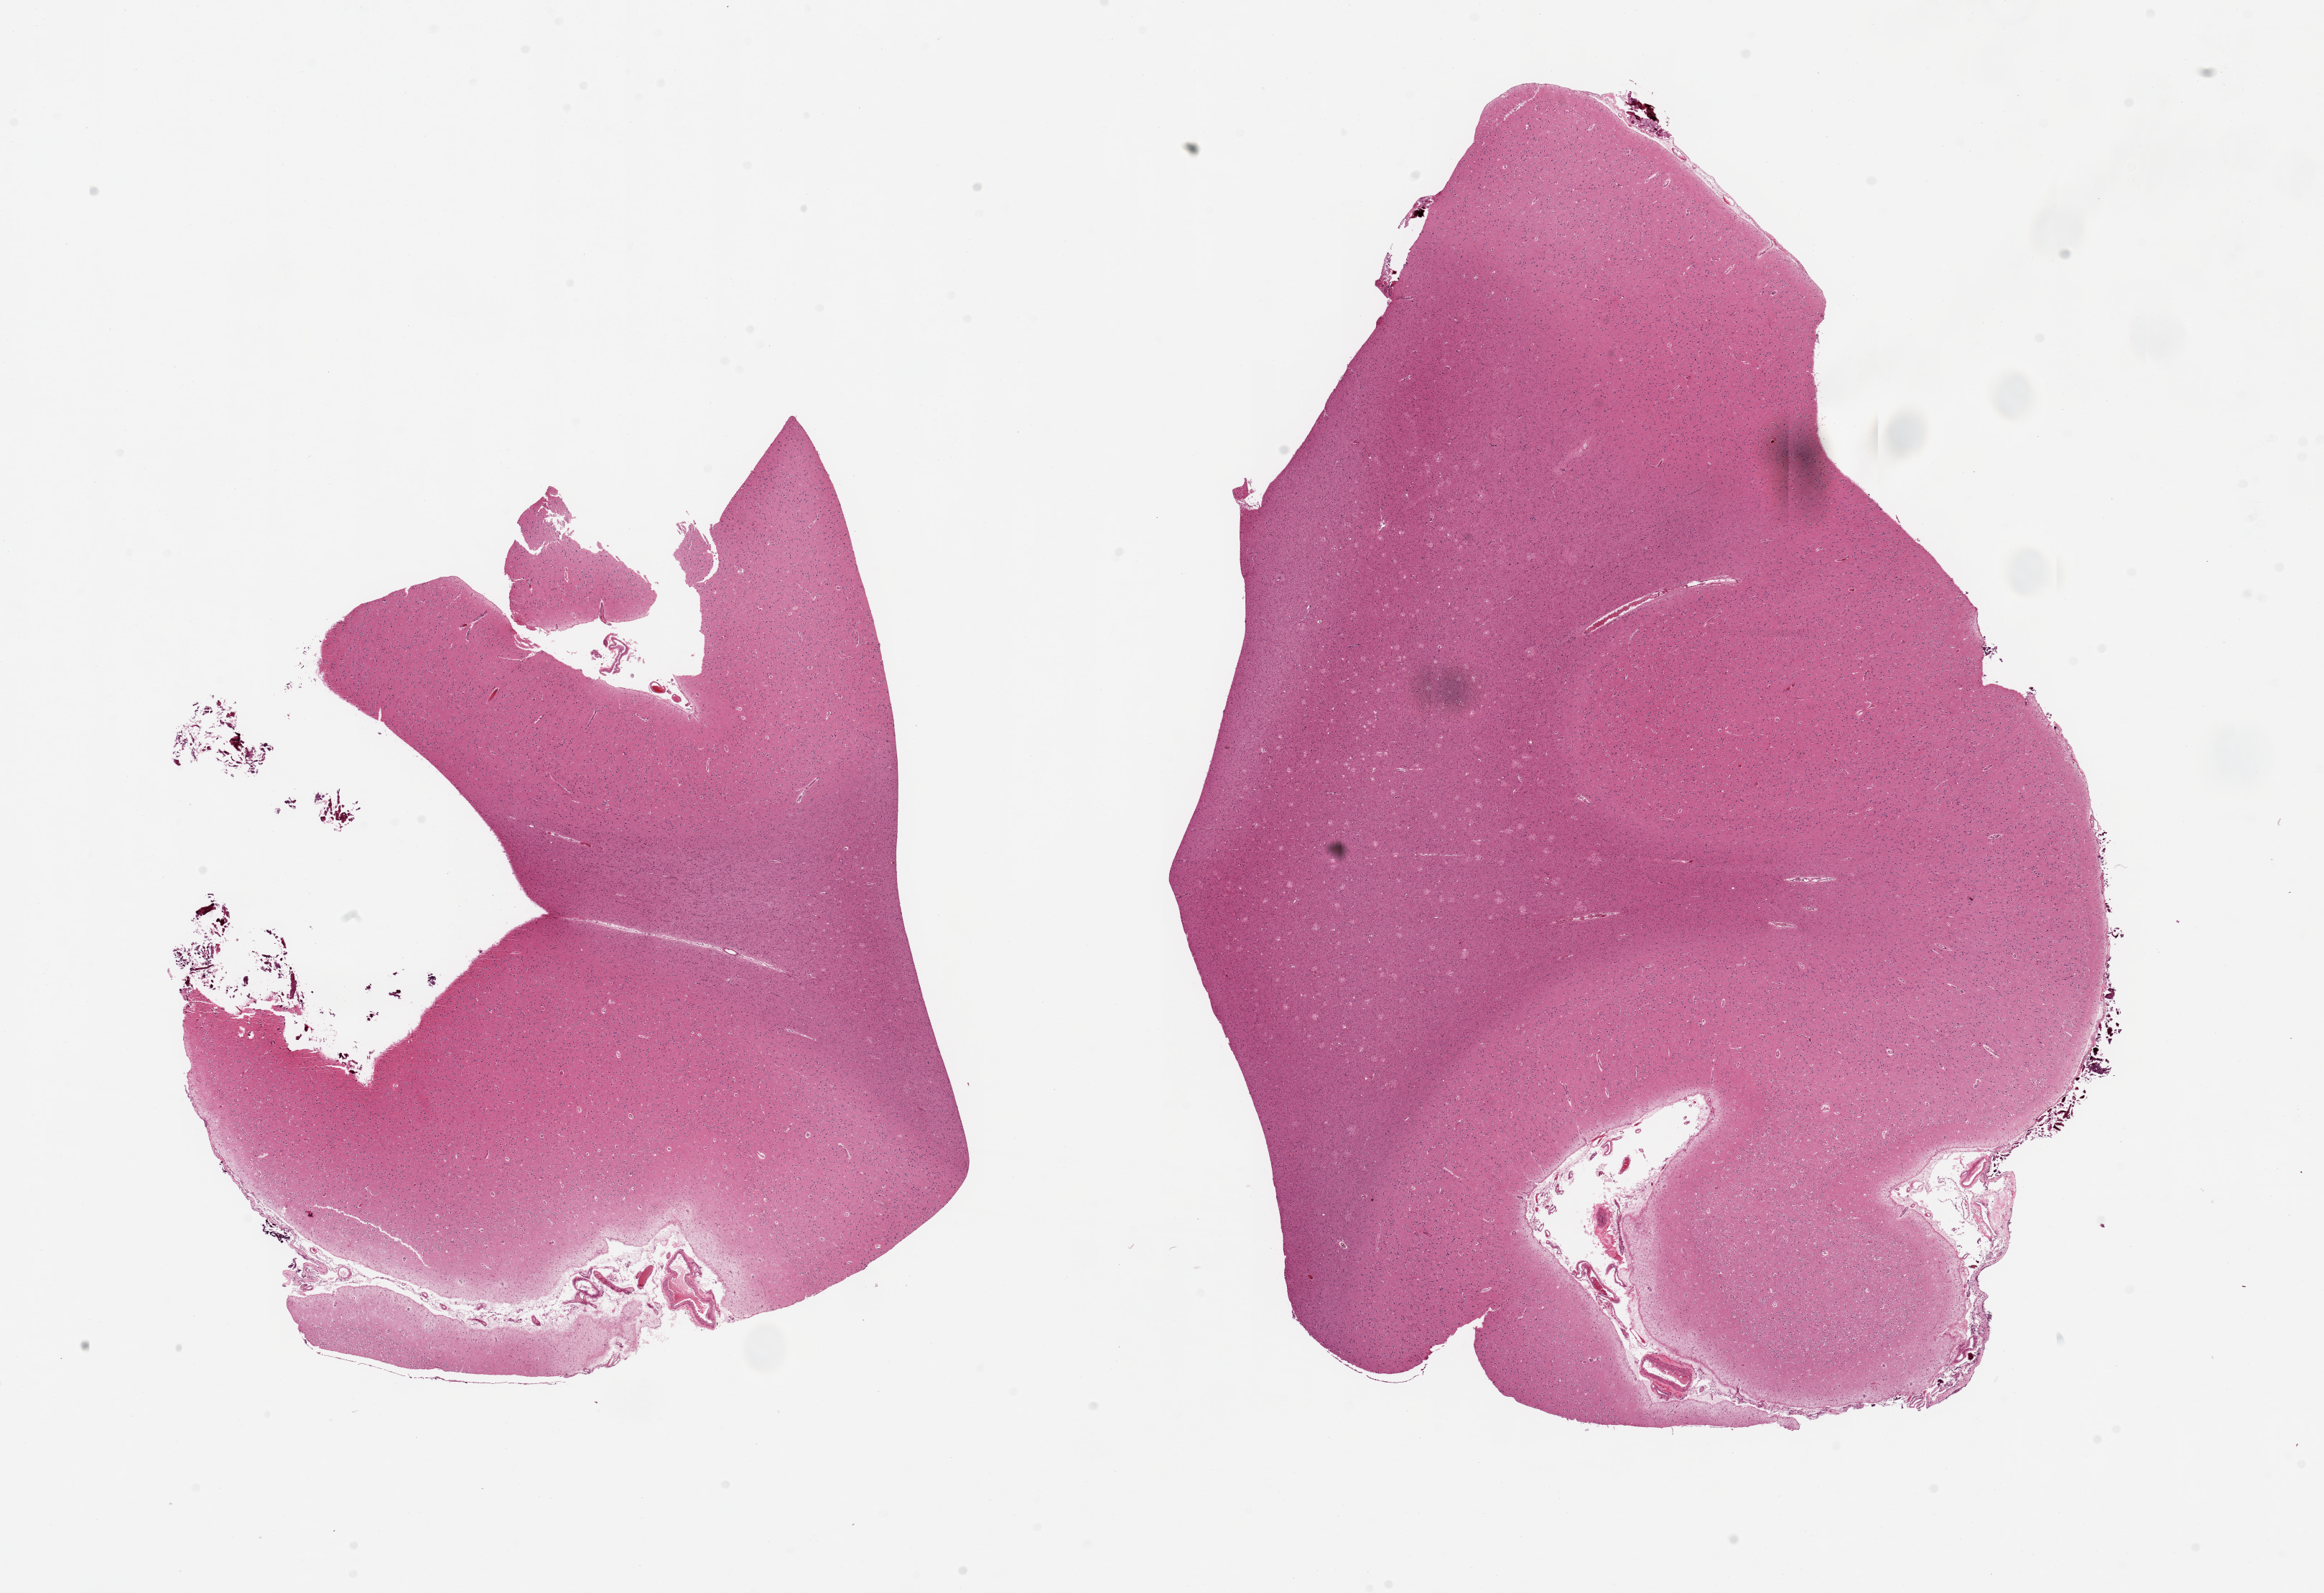
H&E whole-slide image, low-resolution overview of the scanned area, about 25.6 x 17.5 mm; PAXgene-fixed, paraffin-embedded tissue; section of cerebral cortex (target tissue); donor tissue sample. Donor sex: male.
Reviewer comment on this tissue sample: 2 pieces, unusually edematous.